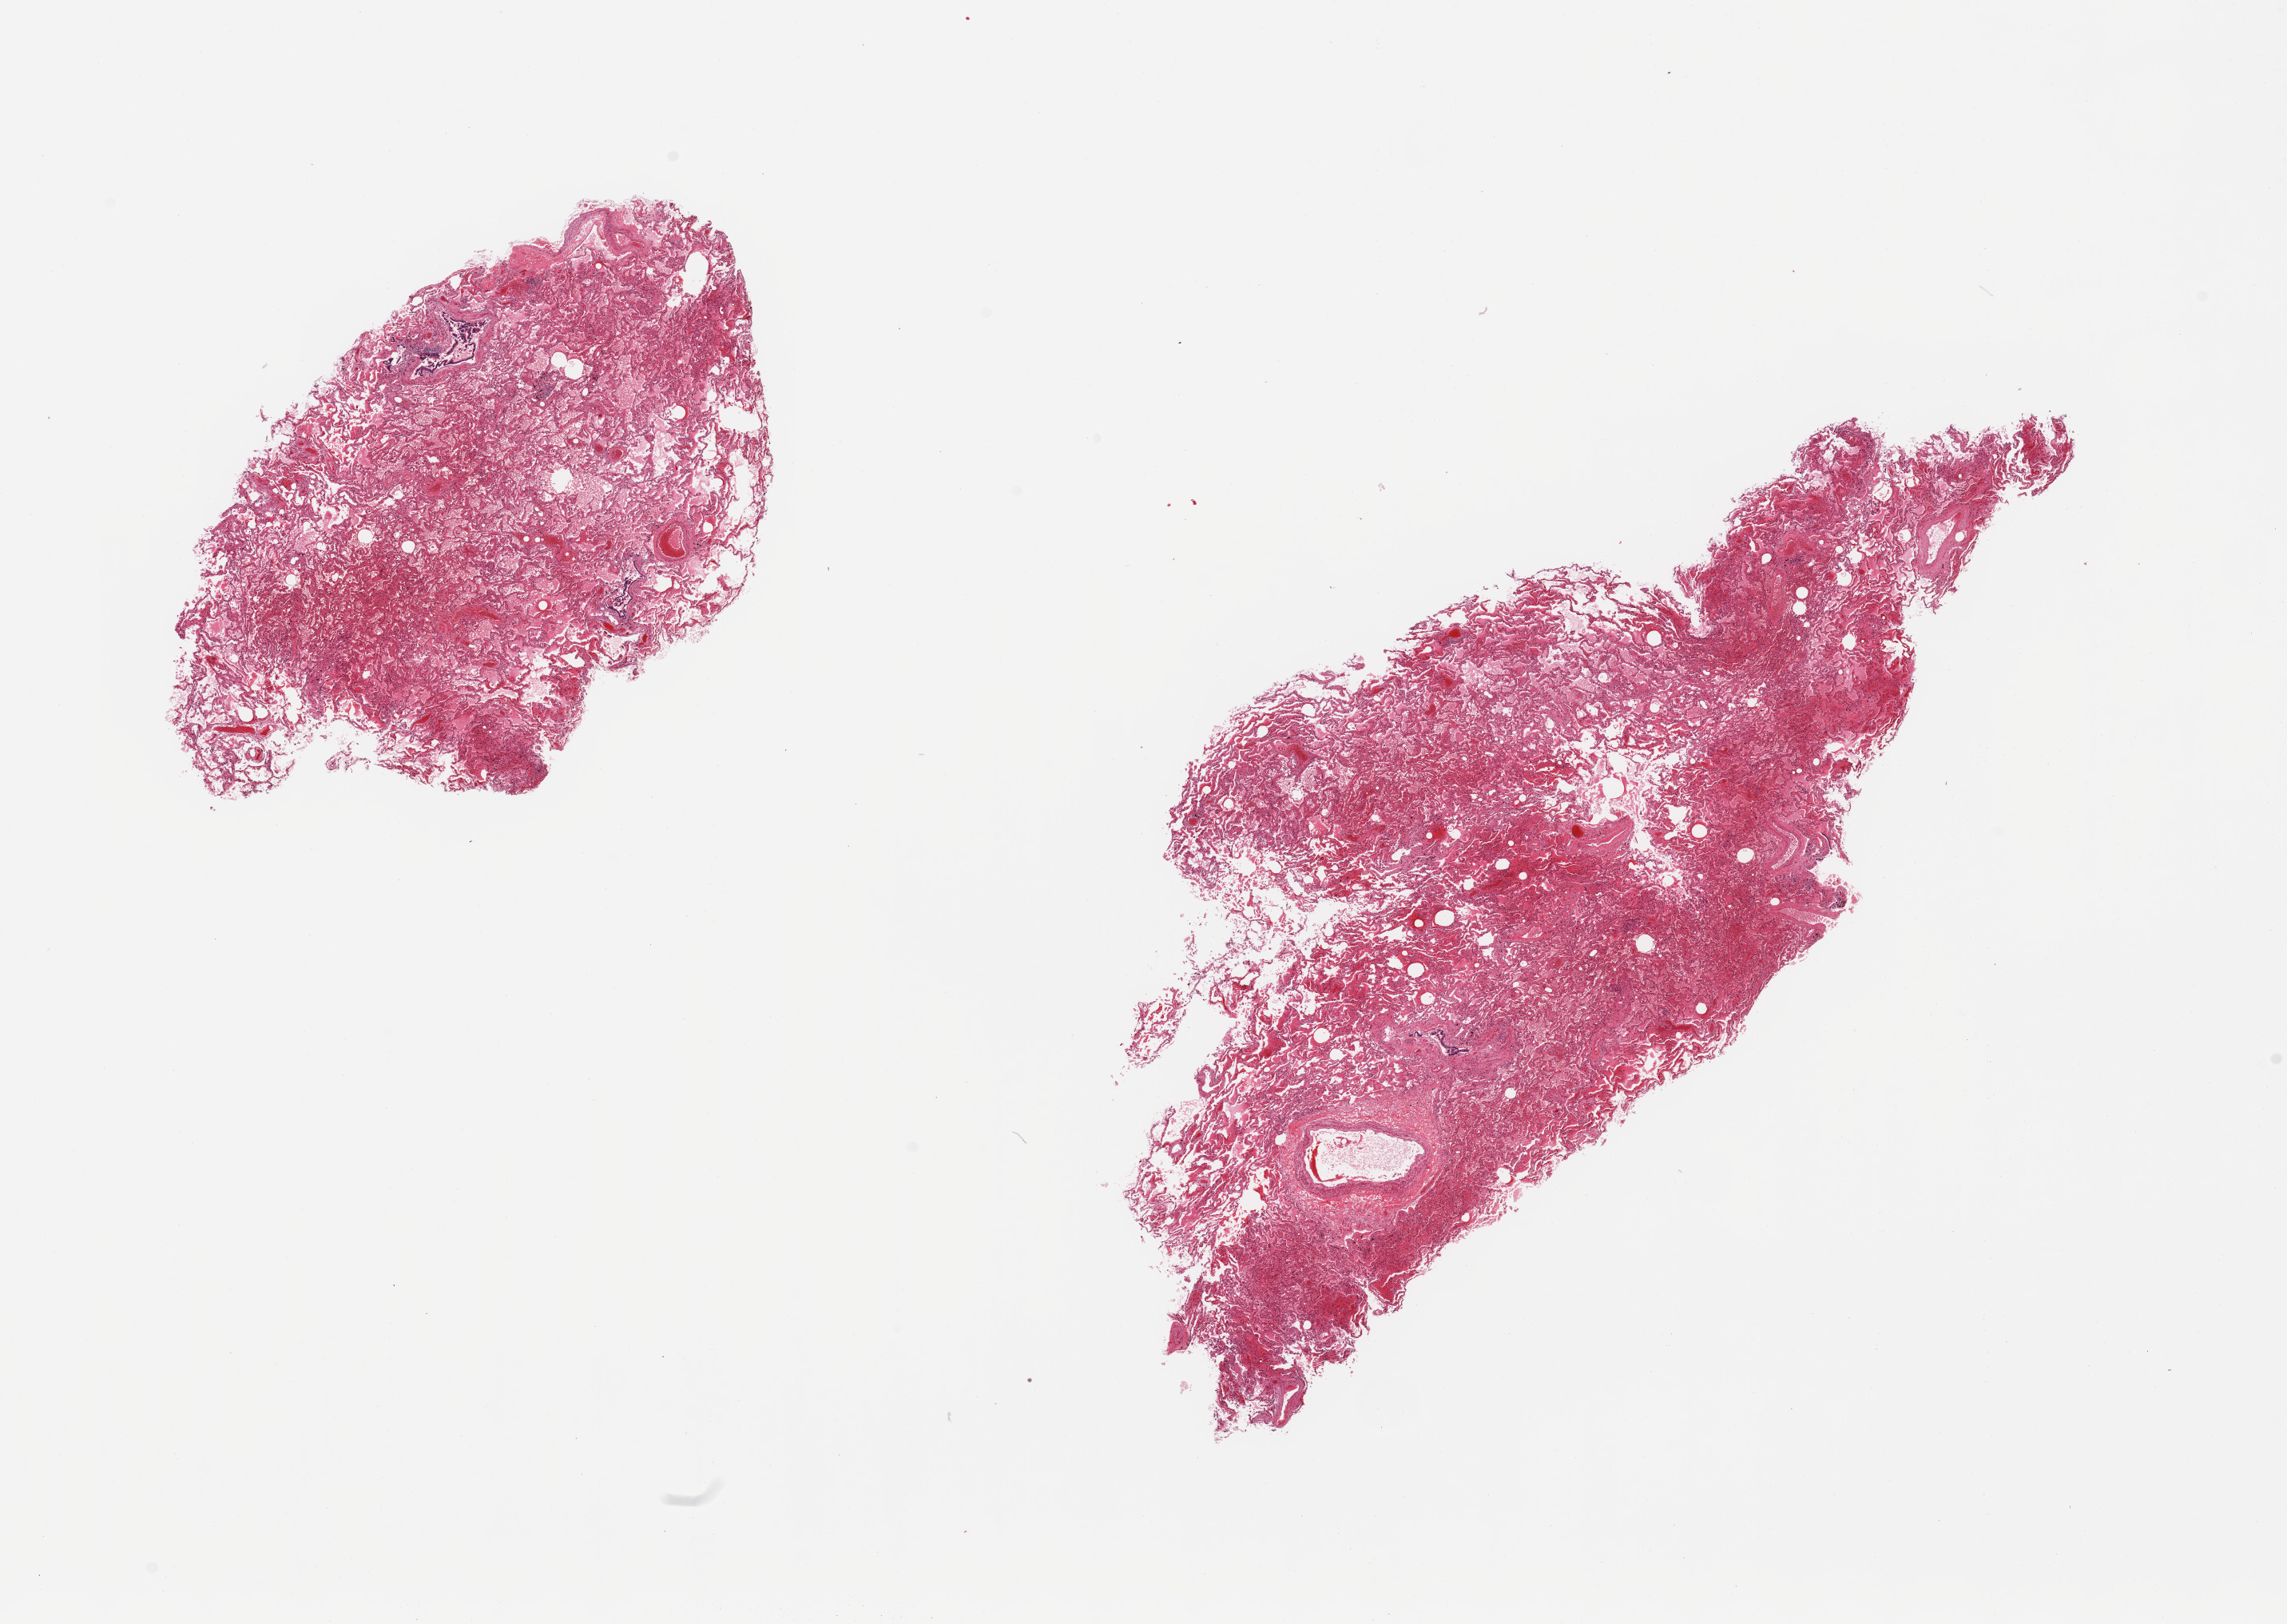
Whole-slide image, haematoxylin and eosin stain, brightfield, a low-resolution overview of the entire scanned area, about 22.6 x 16.1 mm. PAXgene-fixed paraffin-embedded (PFPE) section. Section of lung (target tissue). Donor tissue sample.
Pathologist's review note for this sample: 2 pieces; congestion/edema.